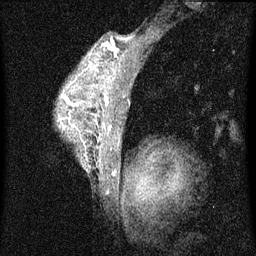
Breast MRI (dynamic contrast-enhanced), one sagittal slice; position 54 of 60 along the scan axis; dynamic contrast-enhanced series, image 2 of 4 at this slice position (ordered by acquisition); 1.5 T; TE 4.2 ms, TR 8 ms; 2 mm slice thickness; 256 × 256 image matrix. Patient: female, 50 years.
Structures marked on this image (semi-automatically segmented with operator editing):
- analysis volume of interest (the breast-tissue region the enhancement analysis was run in; not a lesion): box from (x=60, y=44) to (x=124, y=173) px
- tumour enhancement mask (voxels above the 70 % enhancement threshold inside the analysis volume of interest): (x=106, y=96)–(x=109, y=103)